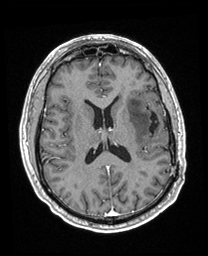
Brain MRI from a brain-tumour surgery series, one axial slice. Position 96 of 208 along the scan axis. T1-weighted post-contrast. 208 × 256 image matrix. From the clinical record (not read from this slice): histopathology: Astrocytoma; WHO grade: 3; IDH mutation: yes; tumour location: Left Insular.
Annotated regions visible in this slice (expert manual segmentation):
- previous resection cavity: bounding box <149,112,160,134> (left, top, right, bottom; pixels)